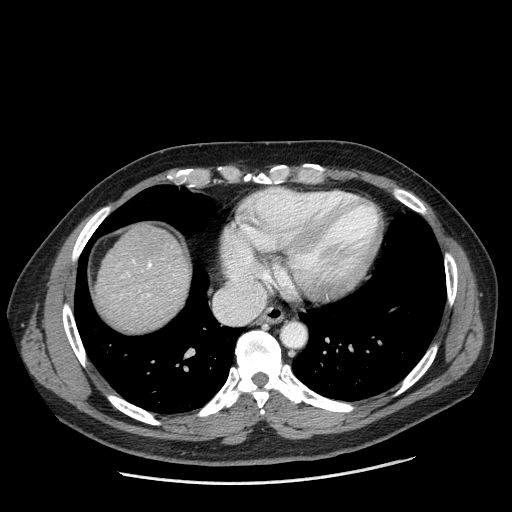
Contrast-enhanced abdominal CT (liver protocol), one axial slice; slice 175 of 198 in the series (ordered by position); reconstruction kernel STANDARD; one of 2 acquisitions stored at this slice position; soft-tissue window (W 400 / L 40 HU); 2.5 mm slice thickness; 512 × 512 image matrix, field of view 400 × 400 mm. From the clinical record (not read from this slice): diagnosis: hepatocellular carcinoma (patient treated with transarterial chemoembolisation; whether this scan precedes or follows treatment is not stated here); TNM stage (as recorded): Stage-II; Child-Pugh class: A; tumour differentiation: moderately differentiated; tumour nodularity: multinodular.
Structures marked on this image (semi-automatically segmented with operator editing):
- liver parenchyma outside the tumour (the mass and vessels are separate outlines, so this box may not span the whole liver): bounding box [x1, y1, x2, y2] px = [96, 222, 190, 330]
- liver vessels: [133, 260, 152, 297]